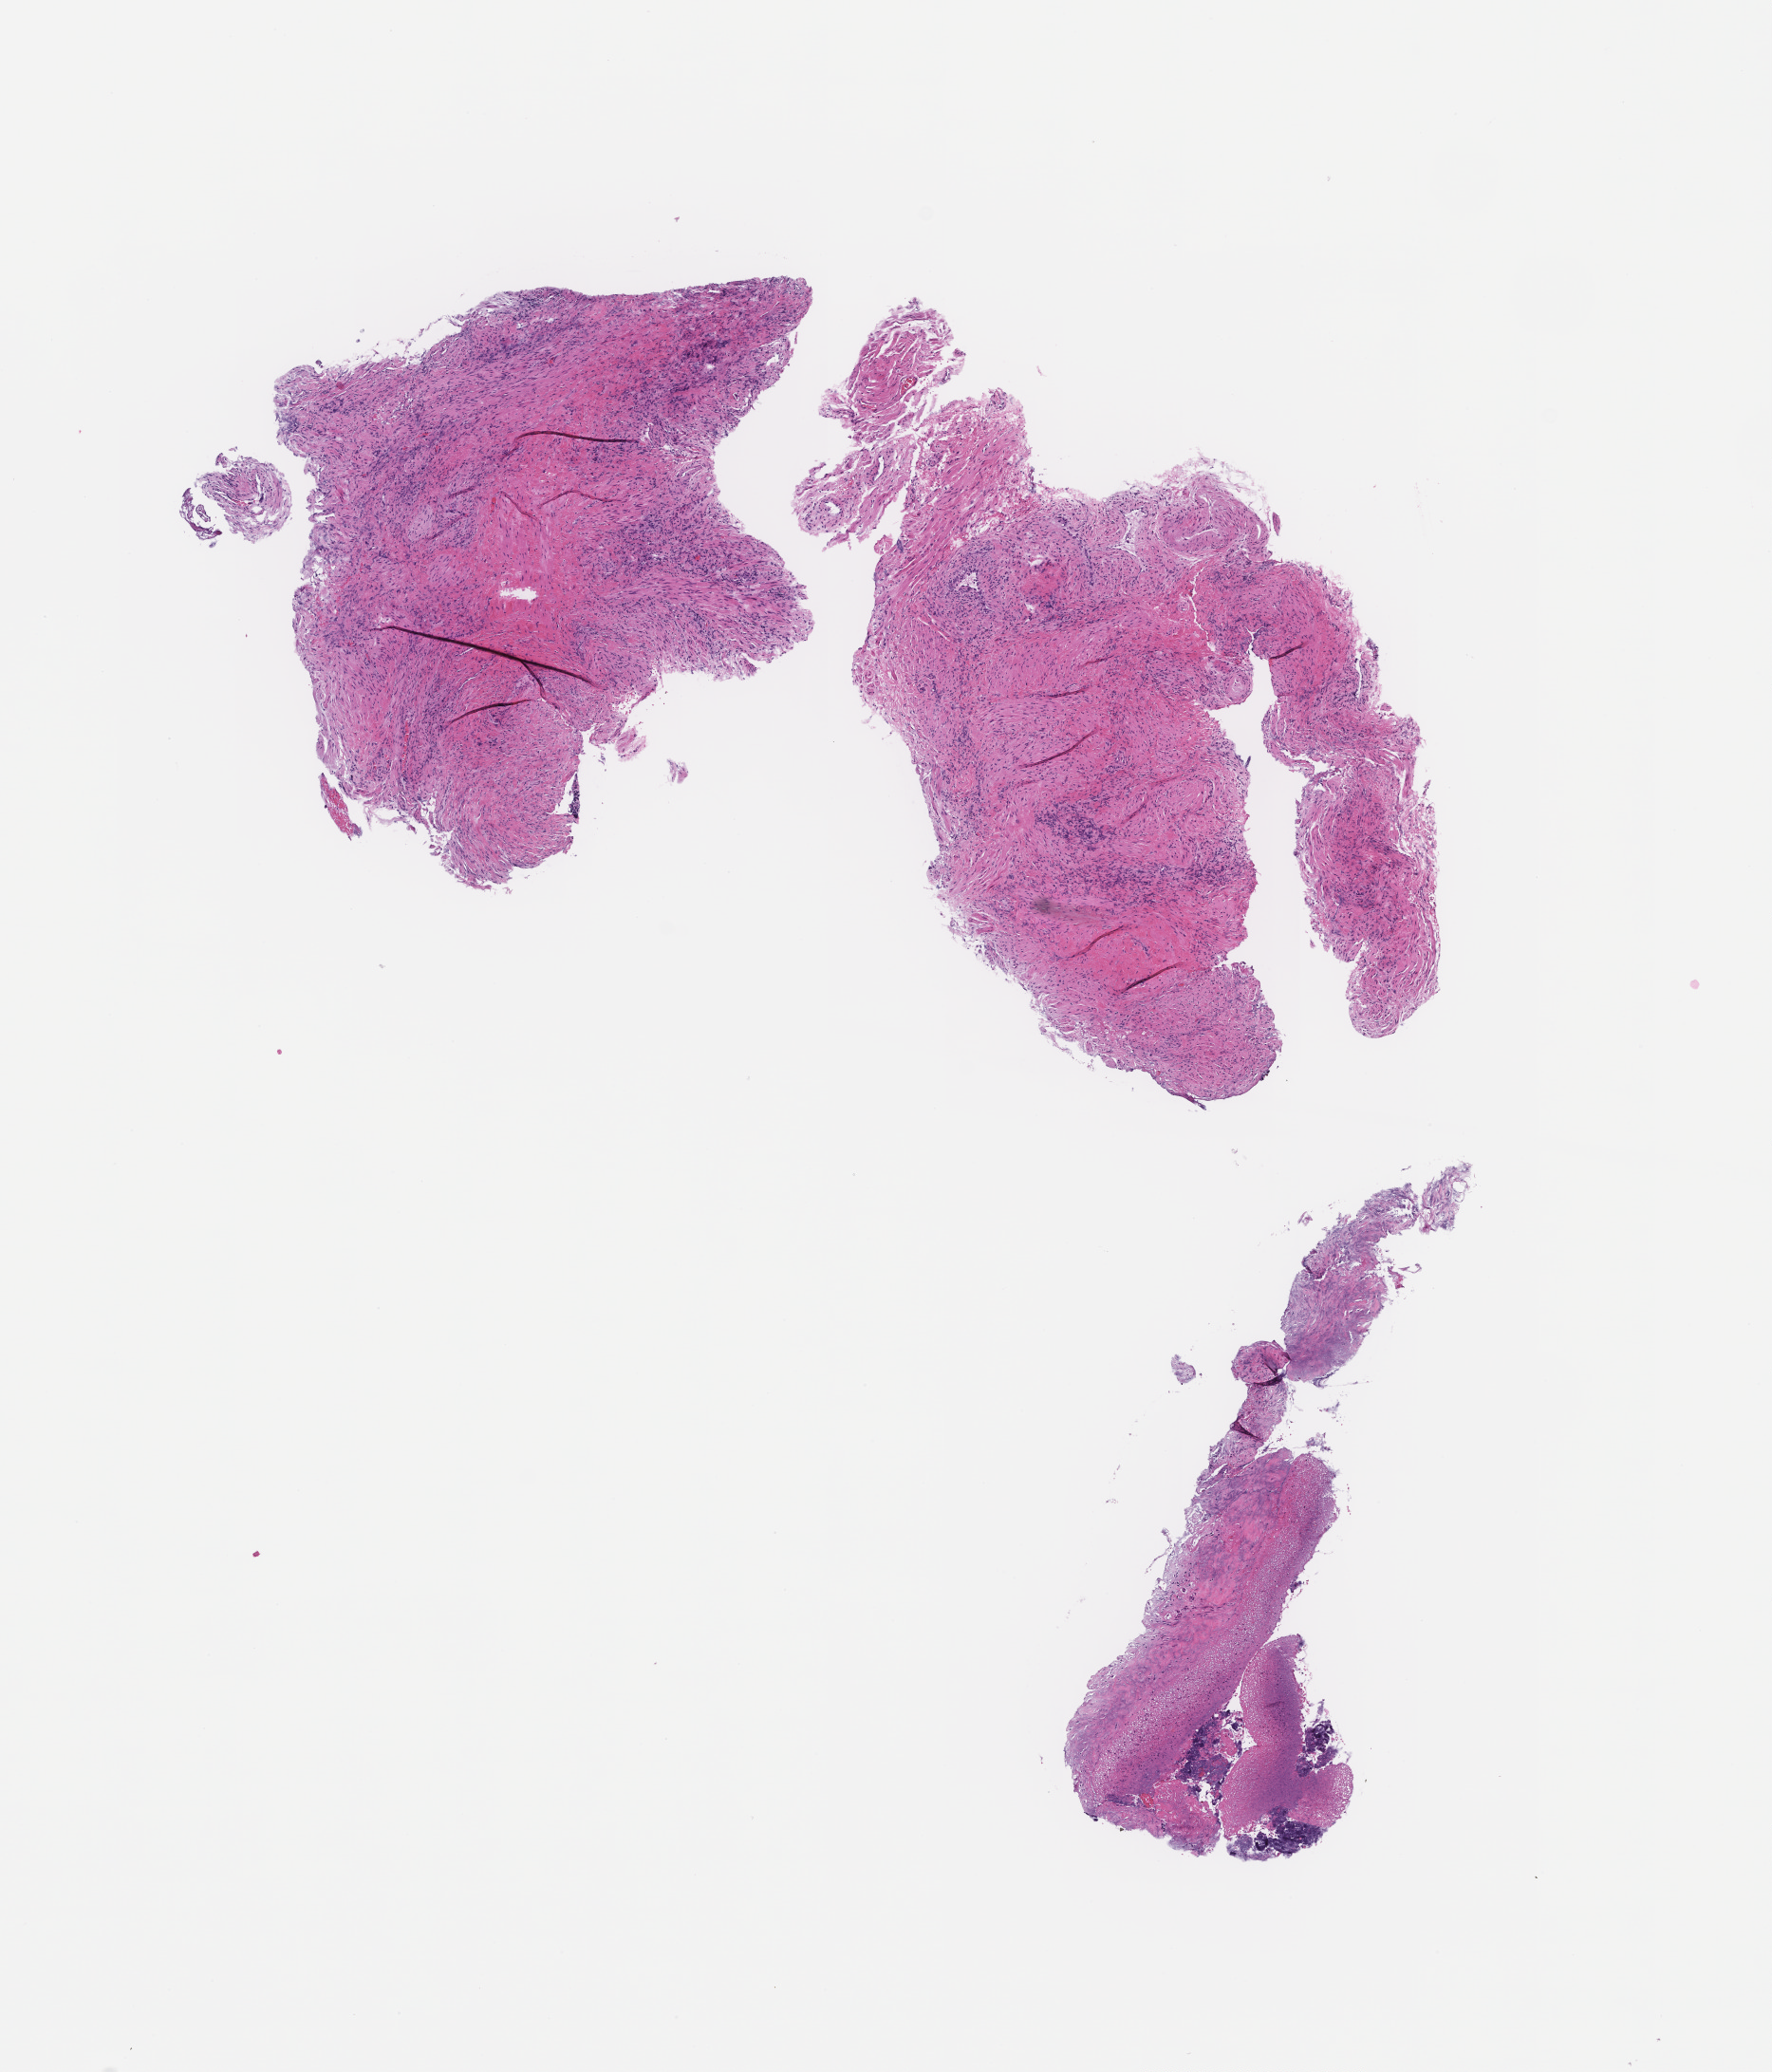
Whole-slide image, H&E stain — a low-resolution overview of the entire scanned area, about 7.5 x 8.8 mm. Formalin-fixed, paraffin-embedded (FFPE) tissue. Patient sex: female.
• this section: metastatic tumor tissue
• patient diagnosis (primary): Ovarian Carcinoma